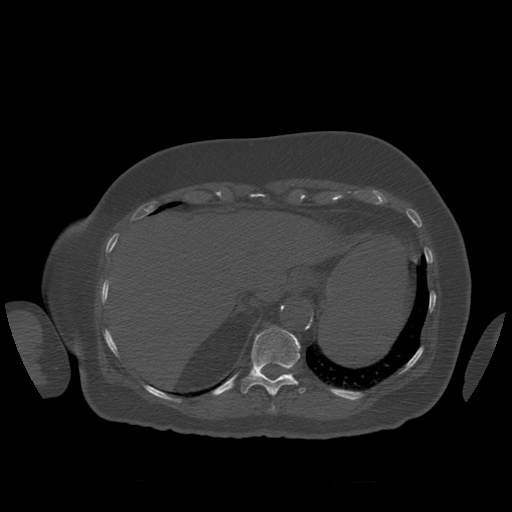
CT including the spine, one axial slice. Slice 322 of 399 in the series (ordered by position). Bone window (W 1800 / L 400 HU). 1.25 mm slice thickness. 512 × 512 image matrix. Patient age 81 years. From the clinical record (not read from this slice): primary cancer: renal.
Structures marked on this image (semi-automatic segmentation, software-assisted and operator-edited):
- T10 vertebra: bounding box <271,406,275,412> (left, top, right, bottom; pixels)
- T11 vertebra: <241,327,306,396>